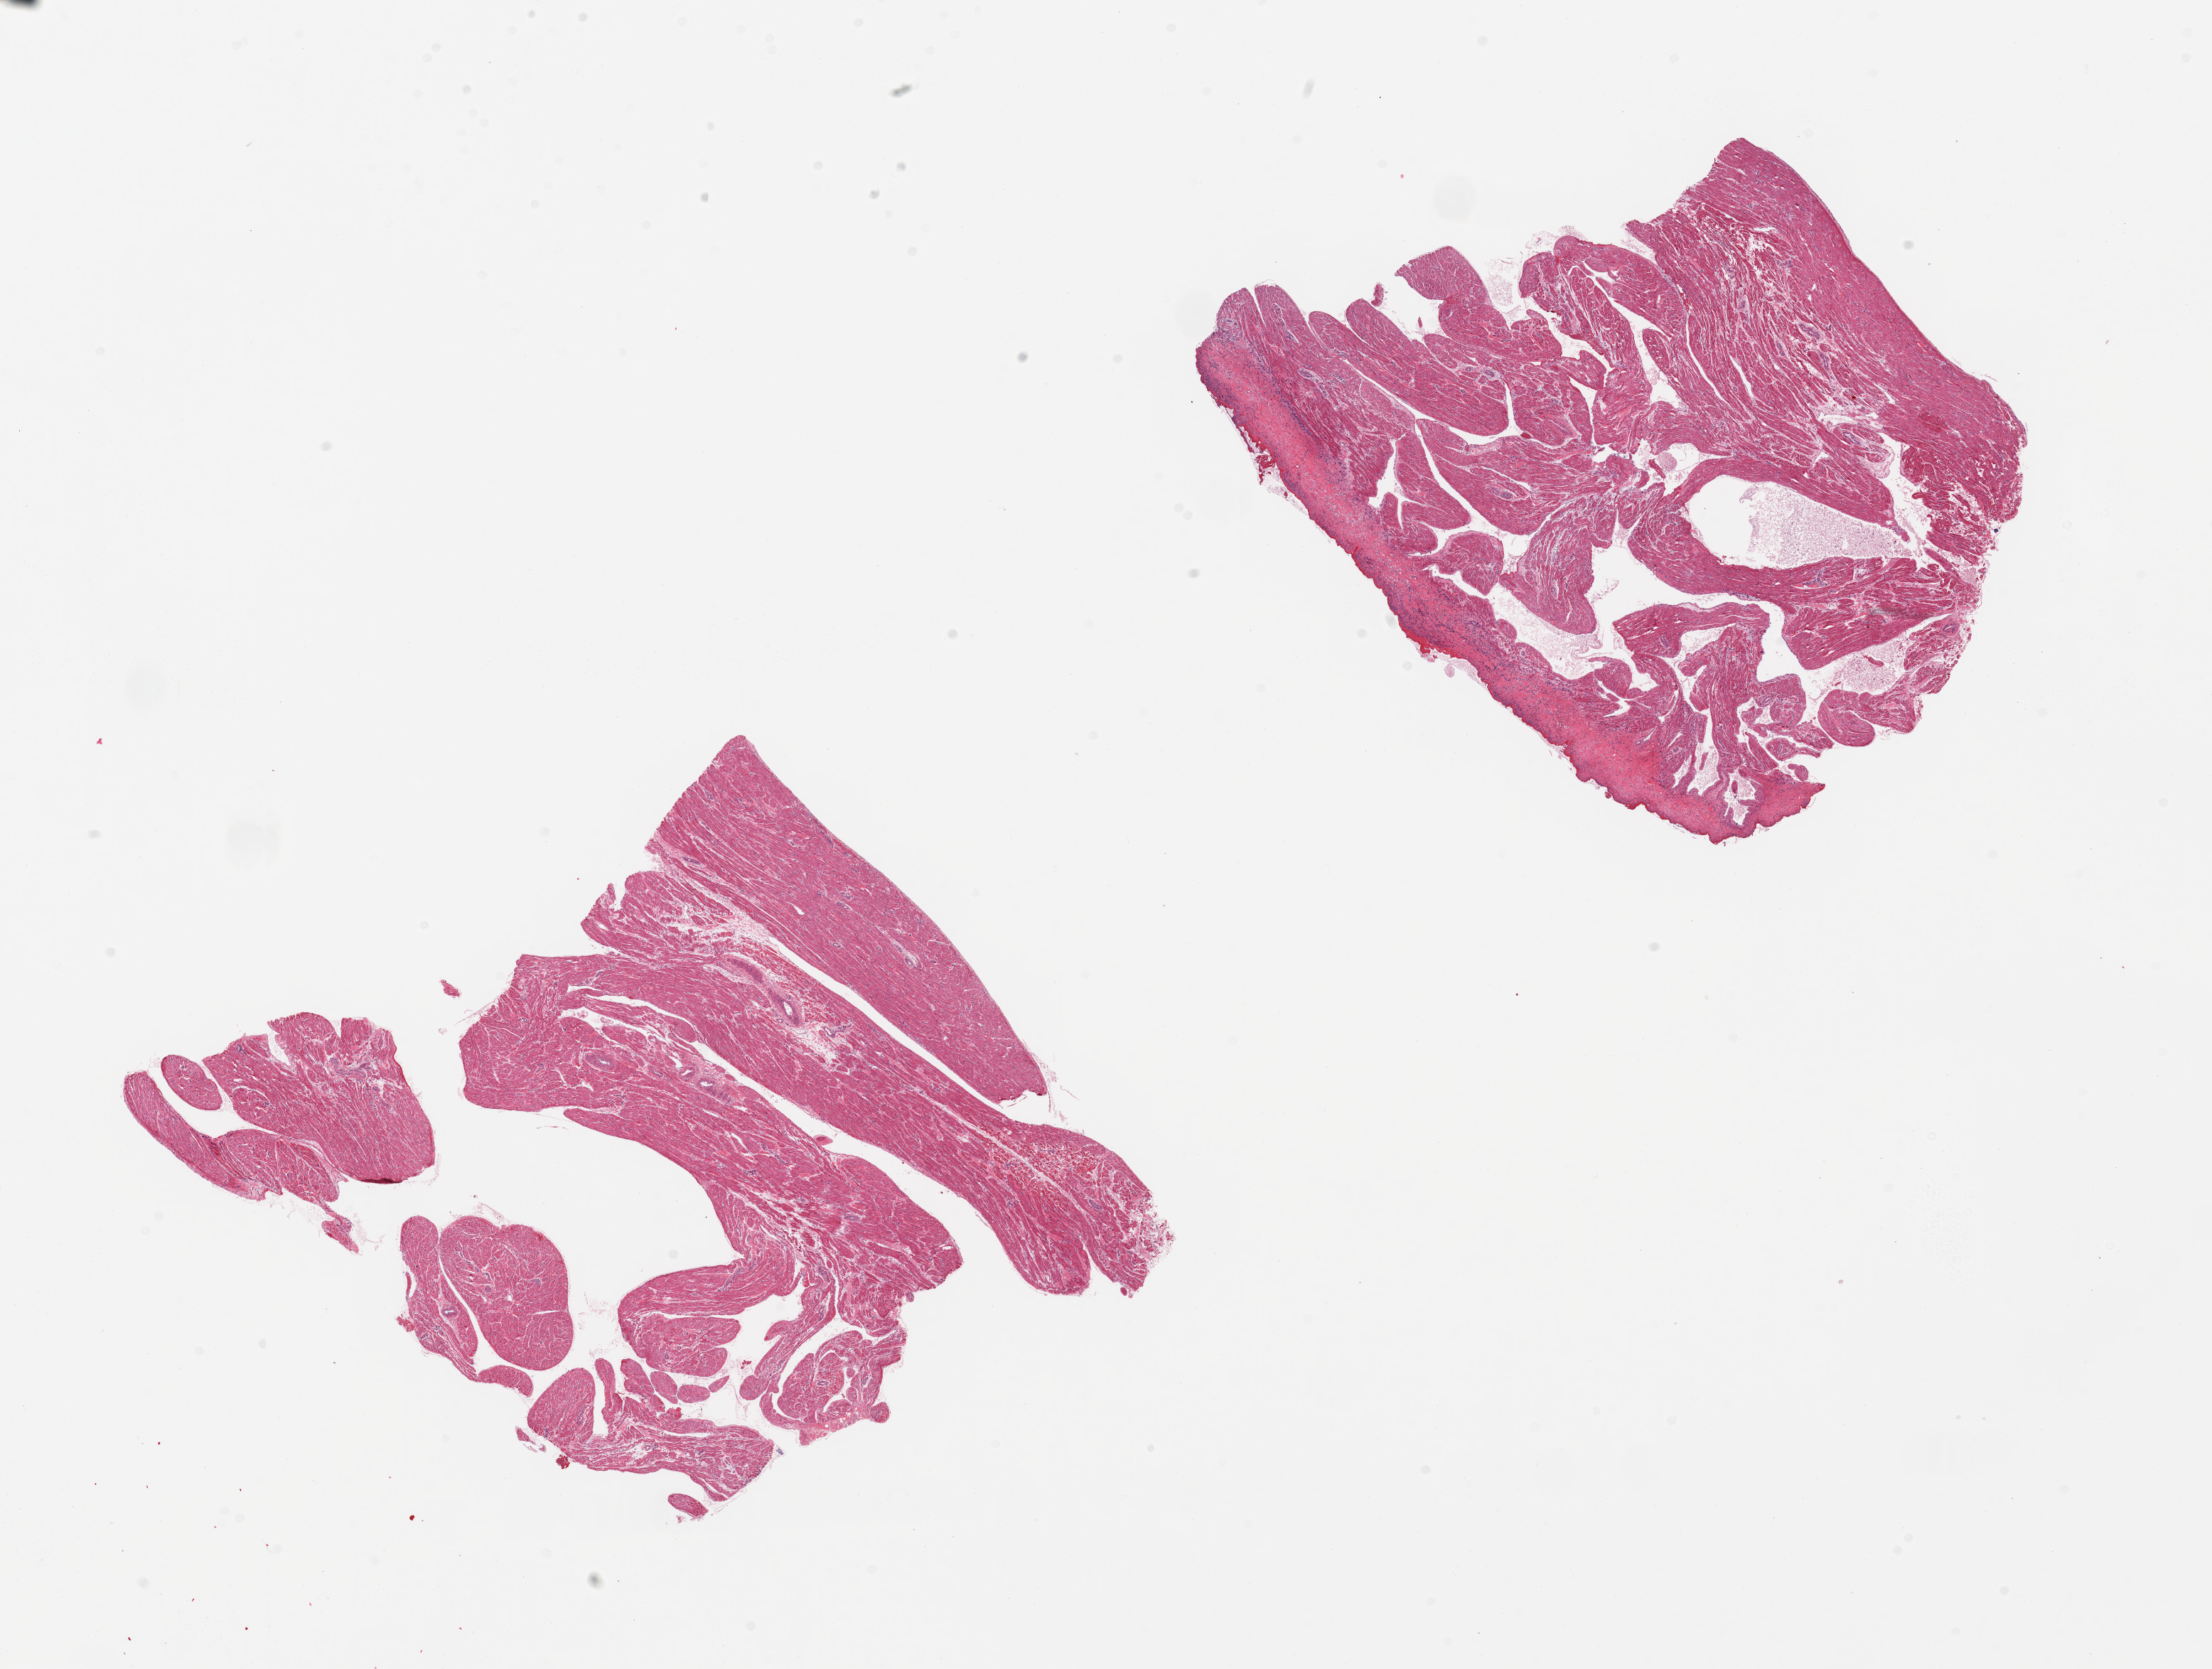
Digitized hematoxylin and eosin (H&E)-stained section, a low-resolution overview of the entire scanned area, about 24.6 x 18.6 mm; PAXgene-fixed paraffin-embedded (PFPE) section; sampled site (target tissue): auricular appendage; tissue donor sample. Donor: female.
Review note (as recorded): 2 pieces, no abnormalities.